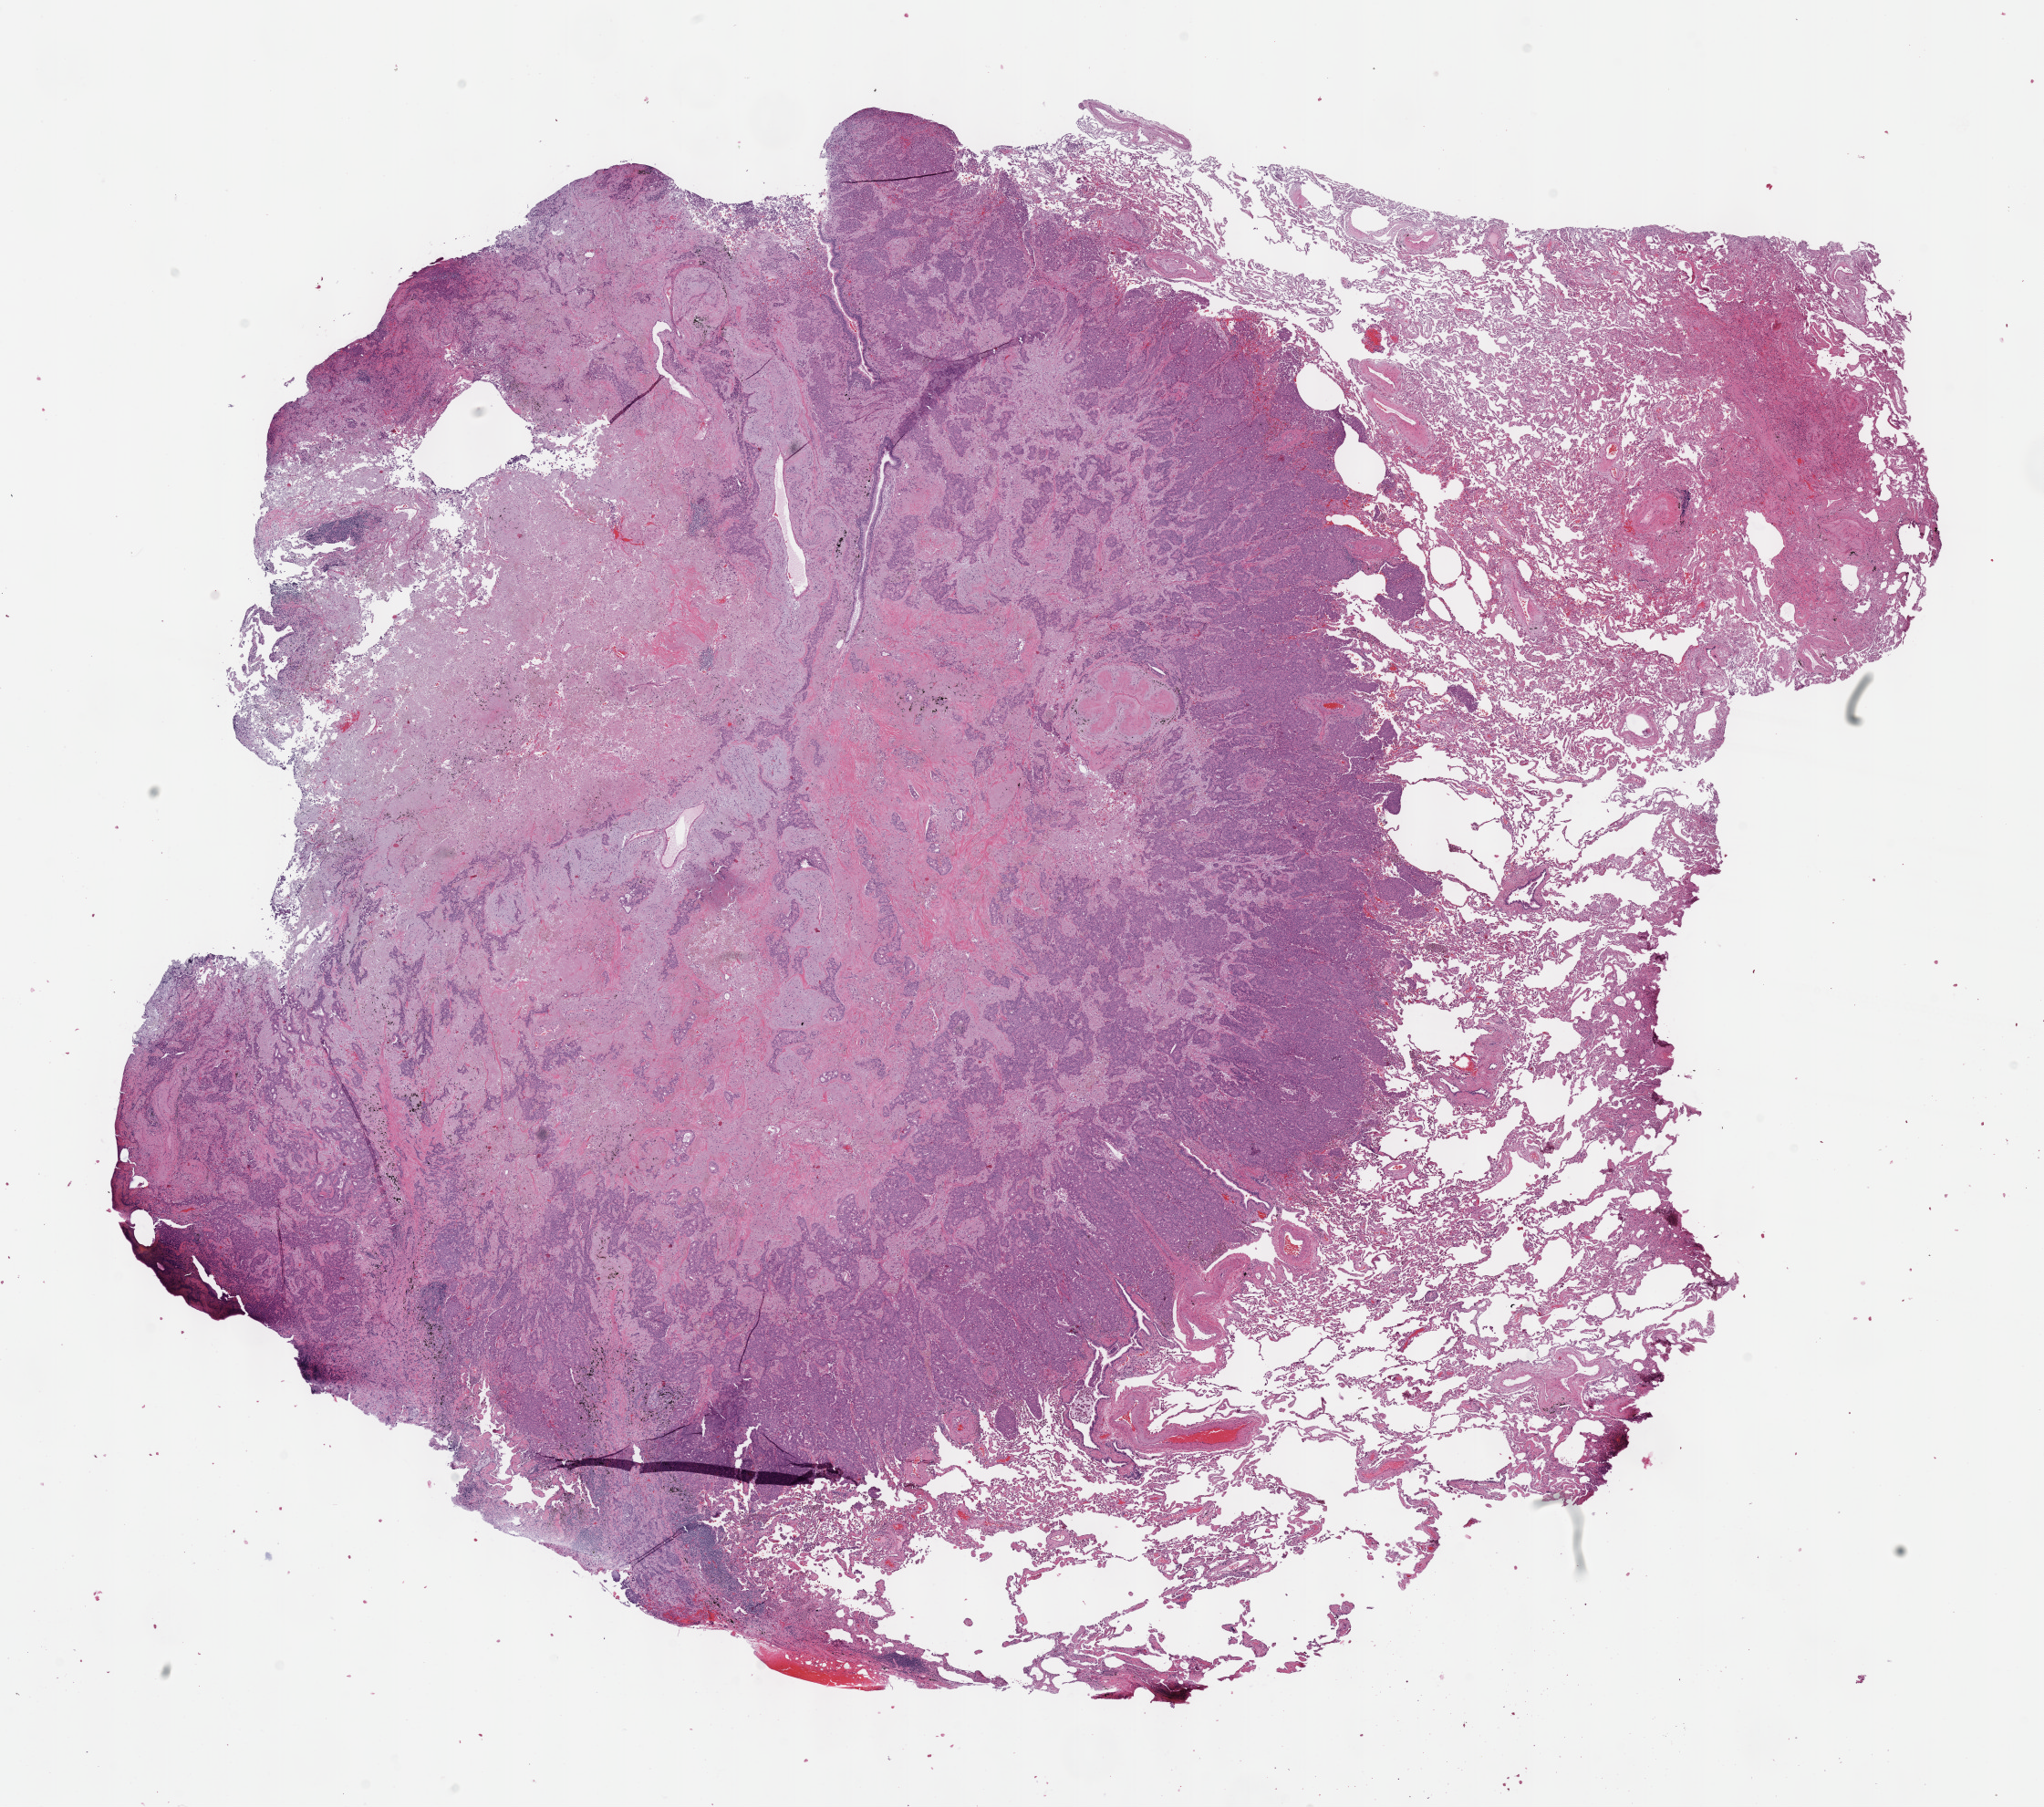
H&E-stained whole-slide image — whole scanned area (about 18.1 x 16.0 mm, acquisition: 40x scan) shown as a low-resolution overview. Formalin-fixed paraffin-embedded (FFPE) diagnostic section. Primary tumour sample from the lung. Female, age 75 years at initial diagnosis.
AJCC pathologic stage: IV (6th edition). Diagnosis: Adenocarcinoma, NOS (lower lobe, lung).